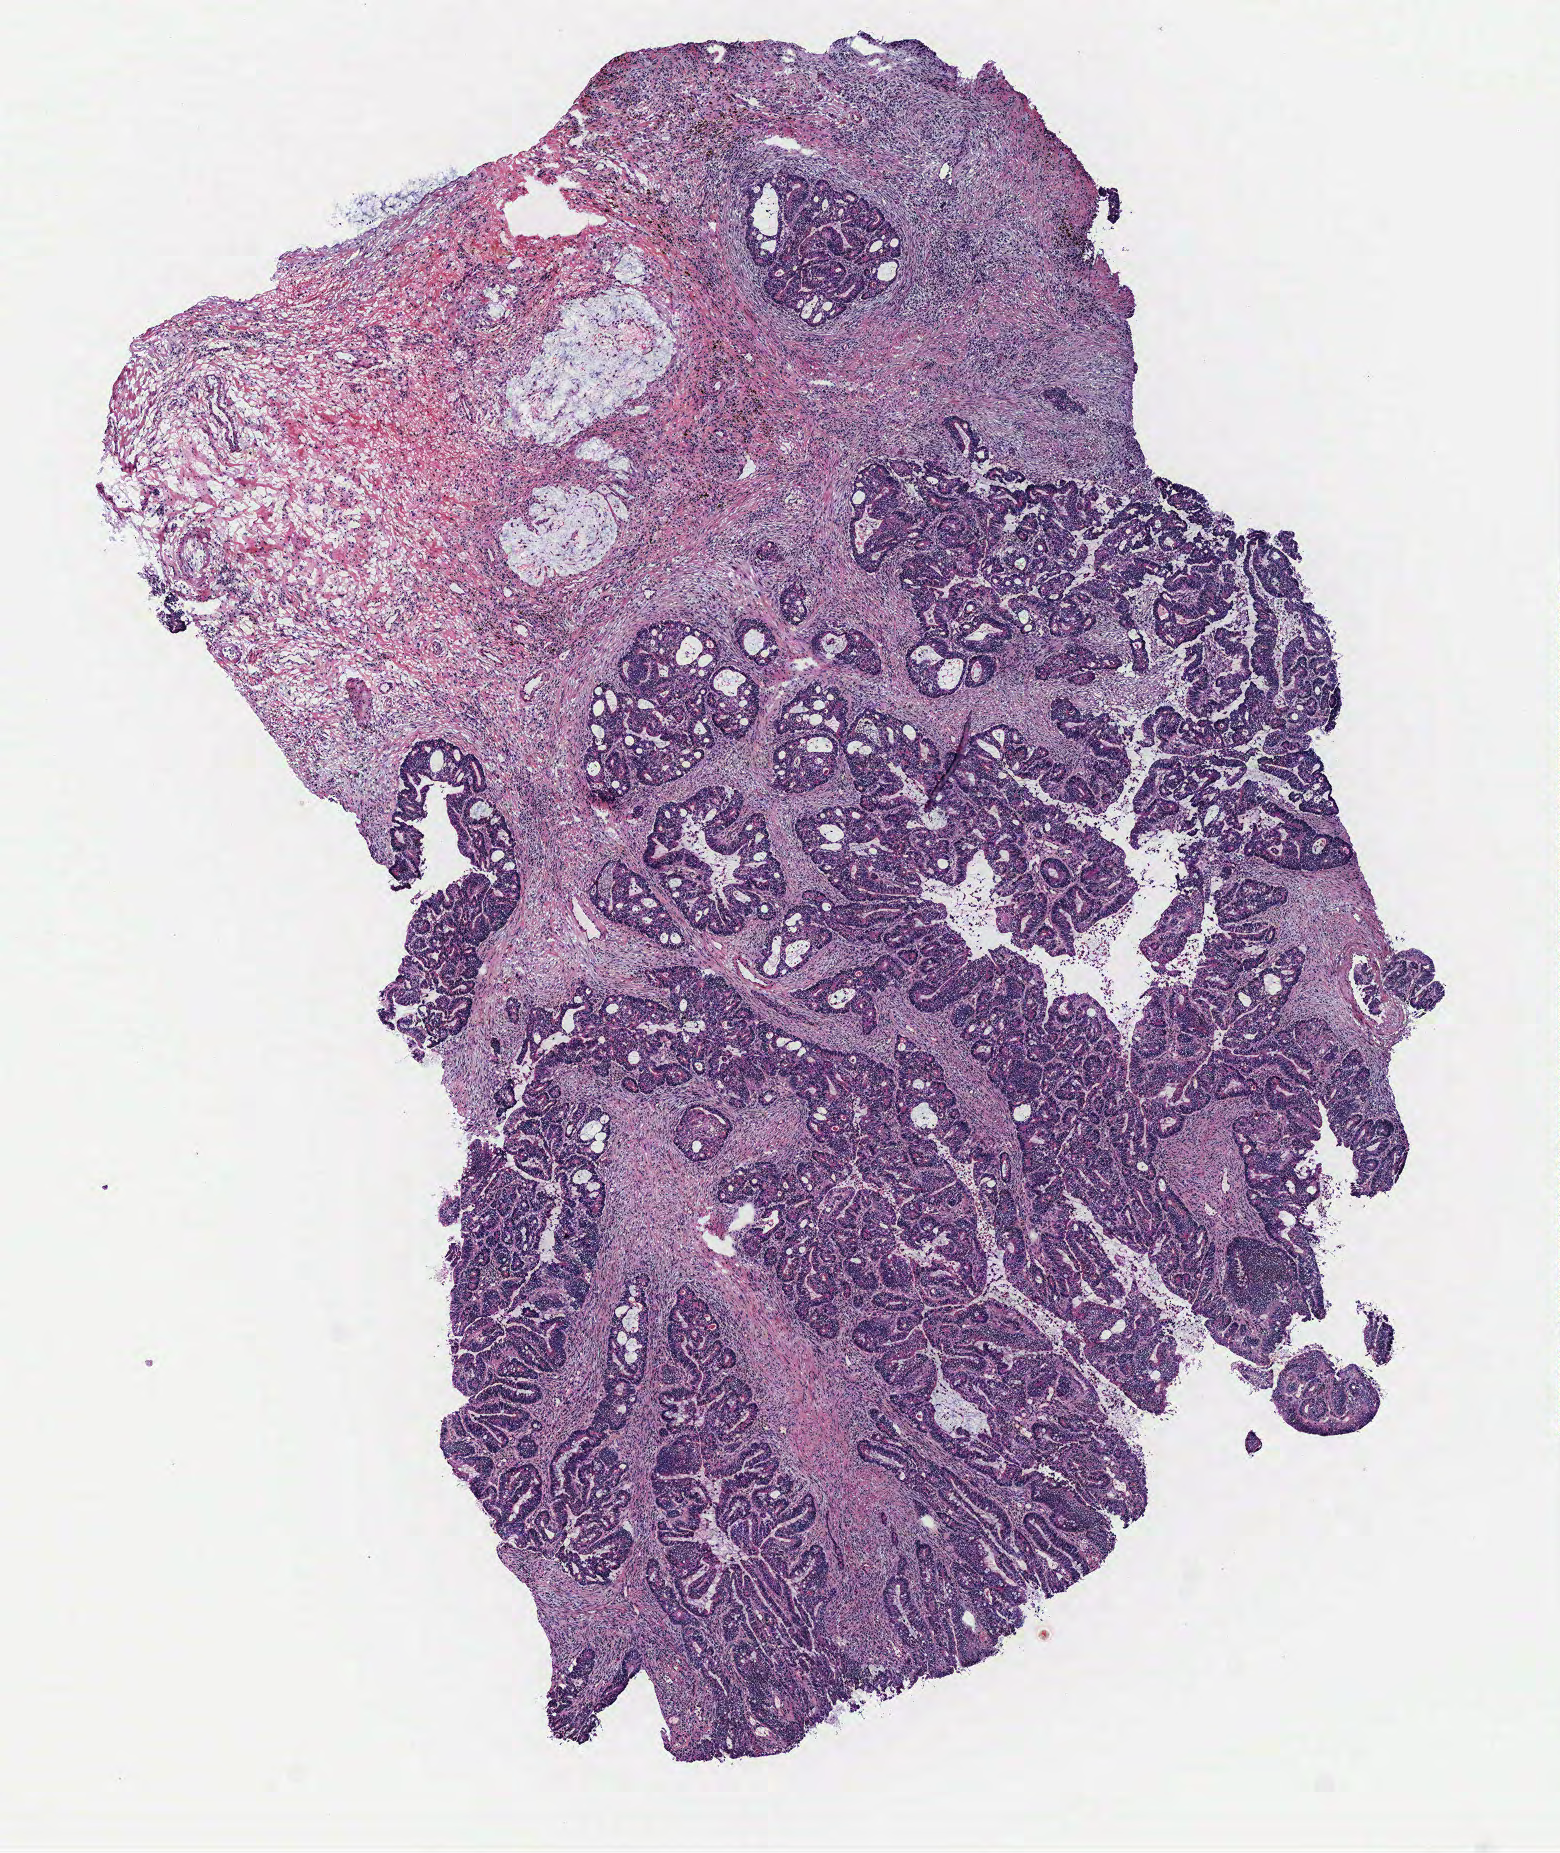
H&E whole-slide image, a low-resolution overview of the entire scanned area, about 6.2 x 7.4 mm (acquisition: 40x scan). Tumour tissue sample, colon. 69-year-old female patient.
• AJCC pathologic stage: IIIB
• histologic diagnosis: Adenocarcinoma, NOS
• primary tumour site (as recorded): colon